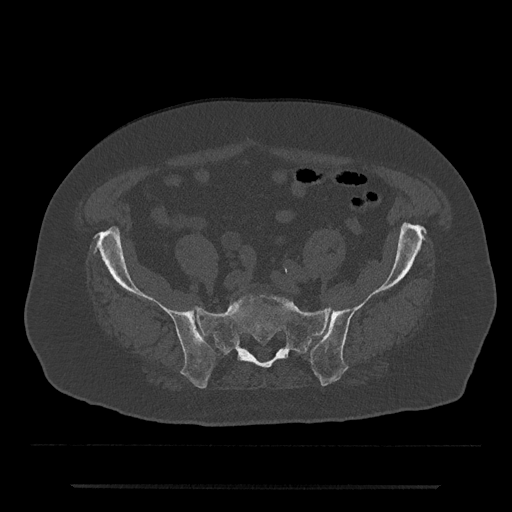
CT including the spine, one axial slice. Position 231 of 797 along the scan axis. Bone window (W 1800 / L 400 HU). 512 × 512 image matrix, field of view 434 × 434 mm. Male patient, age 80 years. From the clinical record (not read from this slice): primary cancer: prostate.
Structures marked on this image (semi-automatically segmented with operator editing):
- L5 vertebra: bounding box (x1, y1, x2, y2) in pixels: (236, 293, 287, 302)